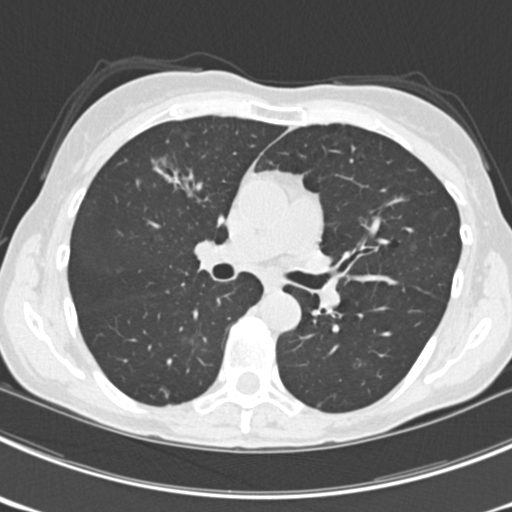
Axial slice from a low-dose chest CT screening exam. Third screening round (two years after baseline). Lung window (W 1500 / L -600 HU). 2 mm slice thickness. Standard (soft-tissue) reconstruction kernel (B30f). 512 × 512 image matrix, field of view 302 × 302 mm. Female, age 63 years at enrolment. Current smoker at enrolment.
- Expert reader's lesion annotation, bounding box [x1, y1, x2, y2] px = [148, 147, 210, 203].
- The screening reader recorded 9 non-calcified nodules or masses ≥4 mm on this exam; which of them this box marks is not recorded.
- Official screen result: positive, other.
- Lung cancer was diagnosed 15 days after this screen: bronchiolo-alveolar adenocarcinoma, NOS, right upper lobe, right middle lobe, right lower lobe, left upper lobe, left lower lobe, moderately differentiated (G2), stage IV (AJCC 6th edition).